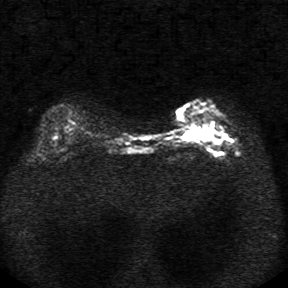
Breast MRI, one axial slice; slice 10 of 34 in the series (ordered by position); diffusion-weighted series; image 2 of 4 stored at this slice position (different b-values; order by instance number); 1.5 T; 5 mm slice thickness; 288 × 288 image matrix. Female patient.
Annotated regions visible in this slice (outlined manually by an expert reader):
- tumour on diffusion-weighted imaging: bounding box <185,124,215,139> (left, top, right, bottom; pixels)